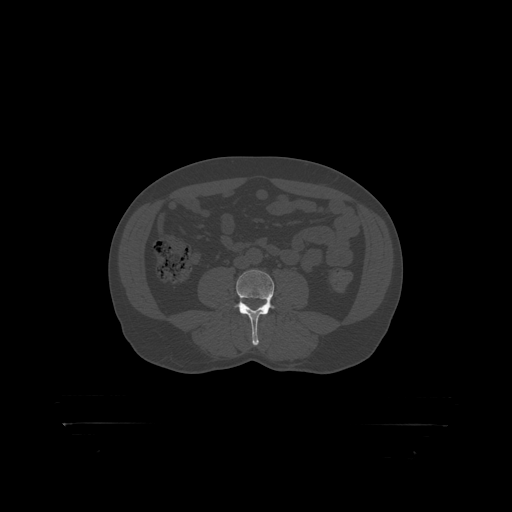
CT including the spine, one axial slice; slice 235 of 399 in the series (ordered by position); reconstruction kernel STANDARD; bone window (W 1800 / L 400 HU); 1.25 mm slice thickness; 512 × 512 image matrix, field of view 650 × 650 mm. Patient: male, 46 years. From the clinical record (not read from this slice): primary cancer: skin.
Outlined on this slice (semi-automatically segmented with operator editing):
- L4 vertebra: bounding box <235,270,275,319> (left, top, right, bottom; pixels)